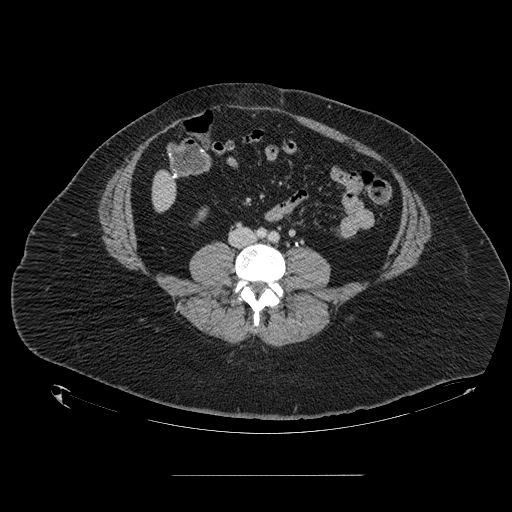
Contrast-enhanced abdominal CT, one axial slice. Position 12 of 164 along the scan axis. Soft-tissue window (W 400 / L 40 HU). 2.5 mm slice thickness. 512 × 512 image matrix. Female patient, age 52 years. Case-level facts recorded for this patient, not image findings: diagnosis: colorectal cancer liver metastases, imaged before liver resection; multiple liver metastases: yes; largest metastasis: 3.5 cm; disease in both lobes: no.
Outlined on this slice (outlined manually by an expert reader):
- liver: bounding box [x1, y1, x2, y2] px = [153, 173, 176, 210]